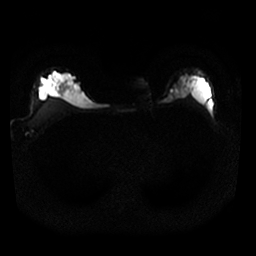
Breast MRI, one axial slice; slice 22 of 25 in the series (ordered by position); diffusion-weighted series; image 2 of 4 stored at this slice position (different b-values; order by instance number); 1.5 T; 4 mm slice thickness; 256 × 256 image matrix, field of view 320 × 320 mm. Female patient.
Annotated regions visible in this slice (manually delineated by an expert):
- tumour on diffusion-weighted imaging: bounding box <173,92,185,99> (left, top, right, bottom; pixels)